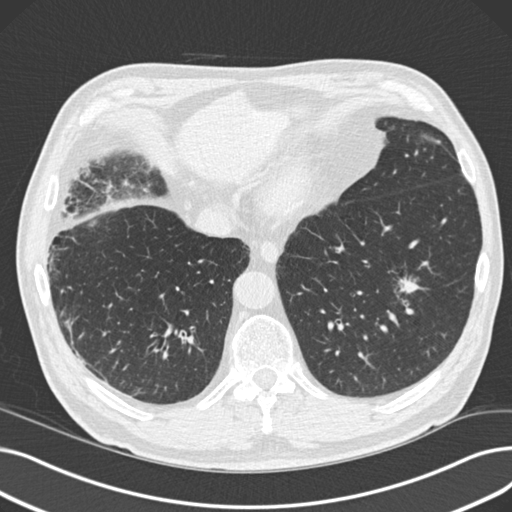
Low-dose screening chest CT, one axial slice; position 38 of 165 along the scan axis; reconstruction kernel B30f; 120 kVp; lung window (W 1500 / L -600 HU); 2 mm slice thickness; 512 × 512 image matrix, field of view 369 × 369 mm.
Structures marked on this image (manually delineated by an expert):
- lesion 1 (tumor, lower lobe of left lung): bounding box (x1, y1, x2, y2) in pixels: (399, 278, 418, 293)